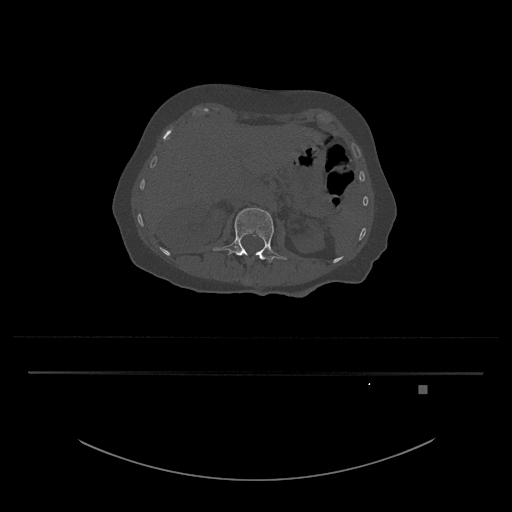
CT including the spine, one axial slice. Position 497 of 797 along the scan axis. Reconstruction kernel Br40s/3. 120 kVp. Bone window (W 1800 / L 400 HU). 0.5 mm slice thickness. 512 × 512 image matrix, field of view 500 × 500 mm. Patient: female, 57 years. From the clinical record (not read from this slice): primary cancer: cervical.
Annotated regions visible in this slice (semi-automatically segmented with operator editing):
- L1 vertebra: bounding box <246,252,259,257> (left, top, right, bottom; pixels)